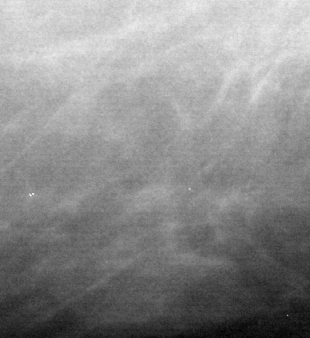
Crop from a digitized film mammogram around one marked abnormality; right breast; MLO view.
- Mass, shape round, margins circumscribed; BI-RADS assessment category 2; subtlety rating 5 on a 1 (subtle) to 5 (obvious) scale; pathology result (as recorded, not read from the image): benign.